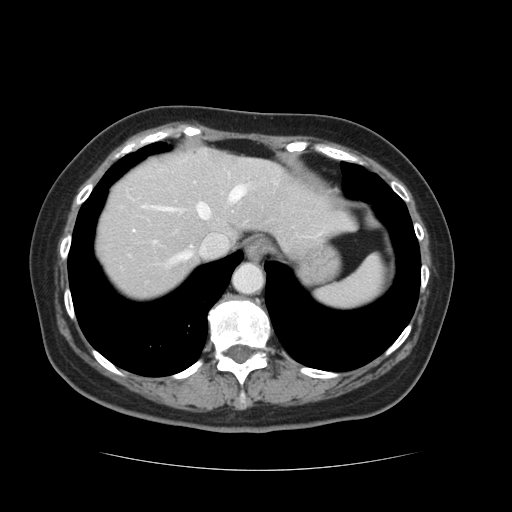
Contrast-enhanced abdominal CT, one axial slice; slice 106 of 128 in the series (ordered by position); intravenous contrast given; soft-tissue window (W 400 / L 40 HU); 2.5 mm slice thickness; 512 × 512 image matrix. Female patient, age 67 years. From the clinical record (not read from this slice): diagnosis: colorectal cancer liver metastases, imaged before liver resection; multiple liver metastases: yes; largest metastasis: 3 cm; chemotherapy before resection: no.
Outlined on this slice (manually delineated by an expert):
- hepatic veins: bounding box [x1, y1, x2, y2] px = [155, 185, 248, 266]
- liver: [95, 148, 349, 301]
- planned liver remnant (the part of the liver to remain after resection): [95, 158, 350, 300]
- portal vein (with intrahepatic branches): [193, 181, 195, 183]